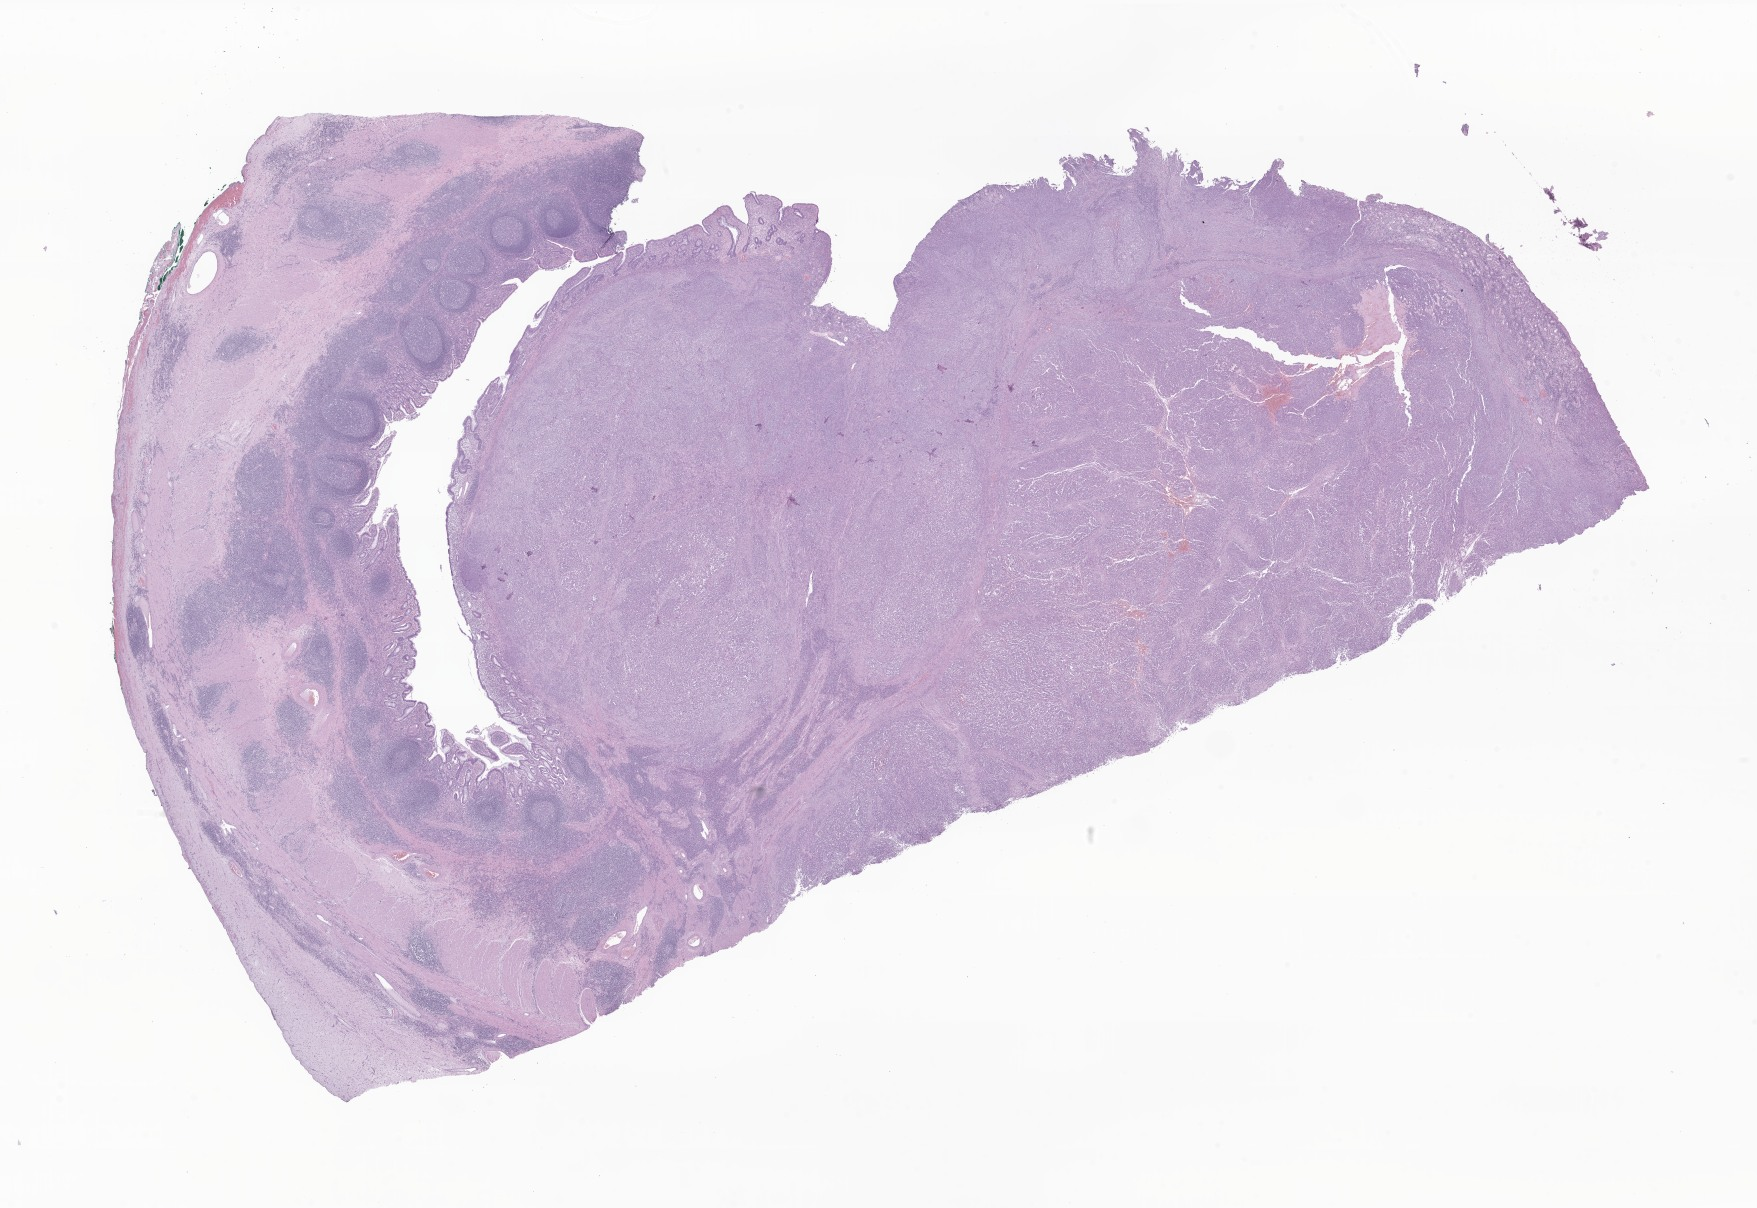
Digitized haematoxylin and eosin-stained section of tumor tissue from the small intestine, whole scanned area (about 29.6 x 20.4 mm) shown as a low-resolution overview; formalin-fixed, paraffin-embedded (FFPE) tissue. Patient: male, age 202 months (16 years 10 months).
* diagnosis (ICD-O-3 morphology term): Ewing sarcoma